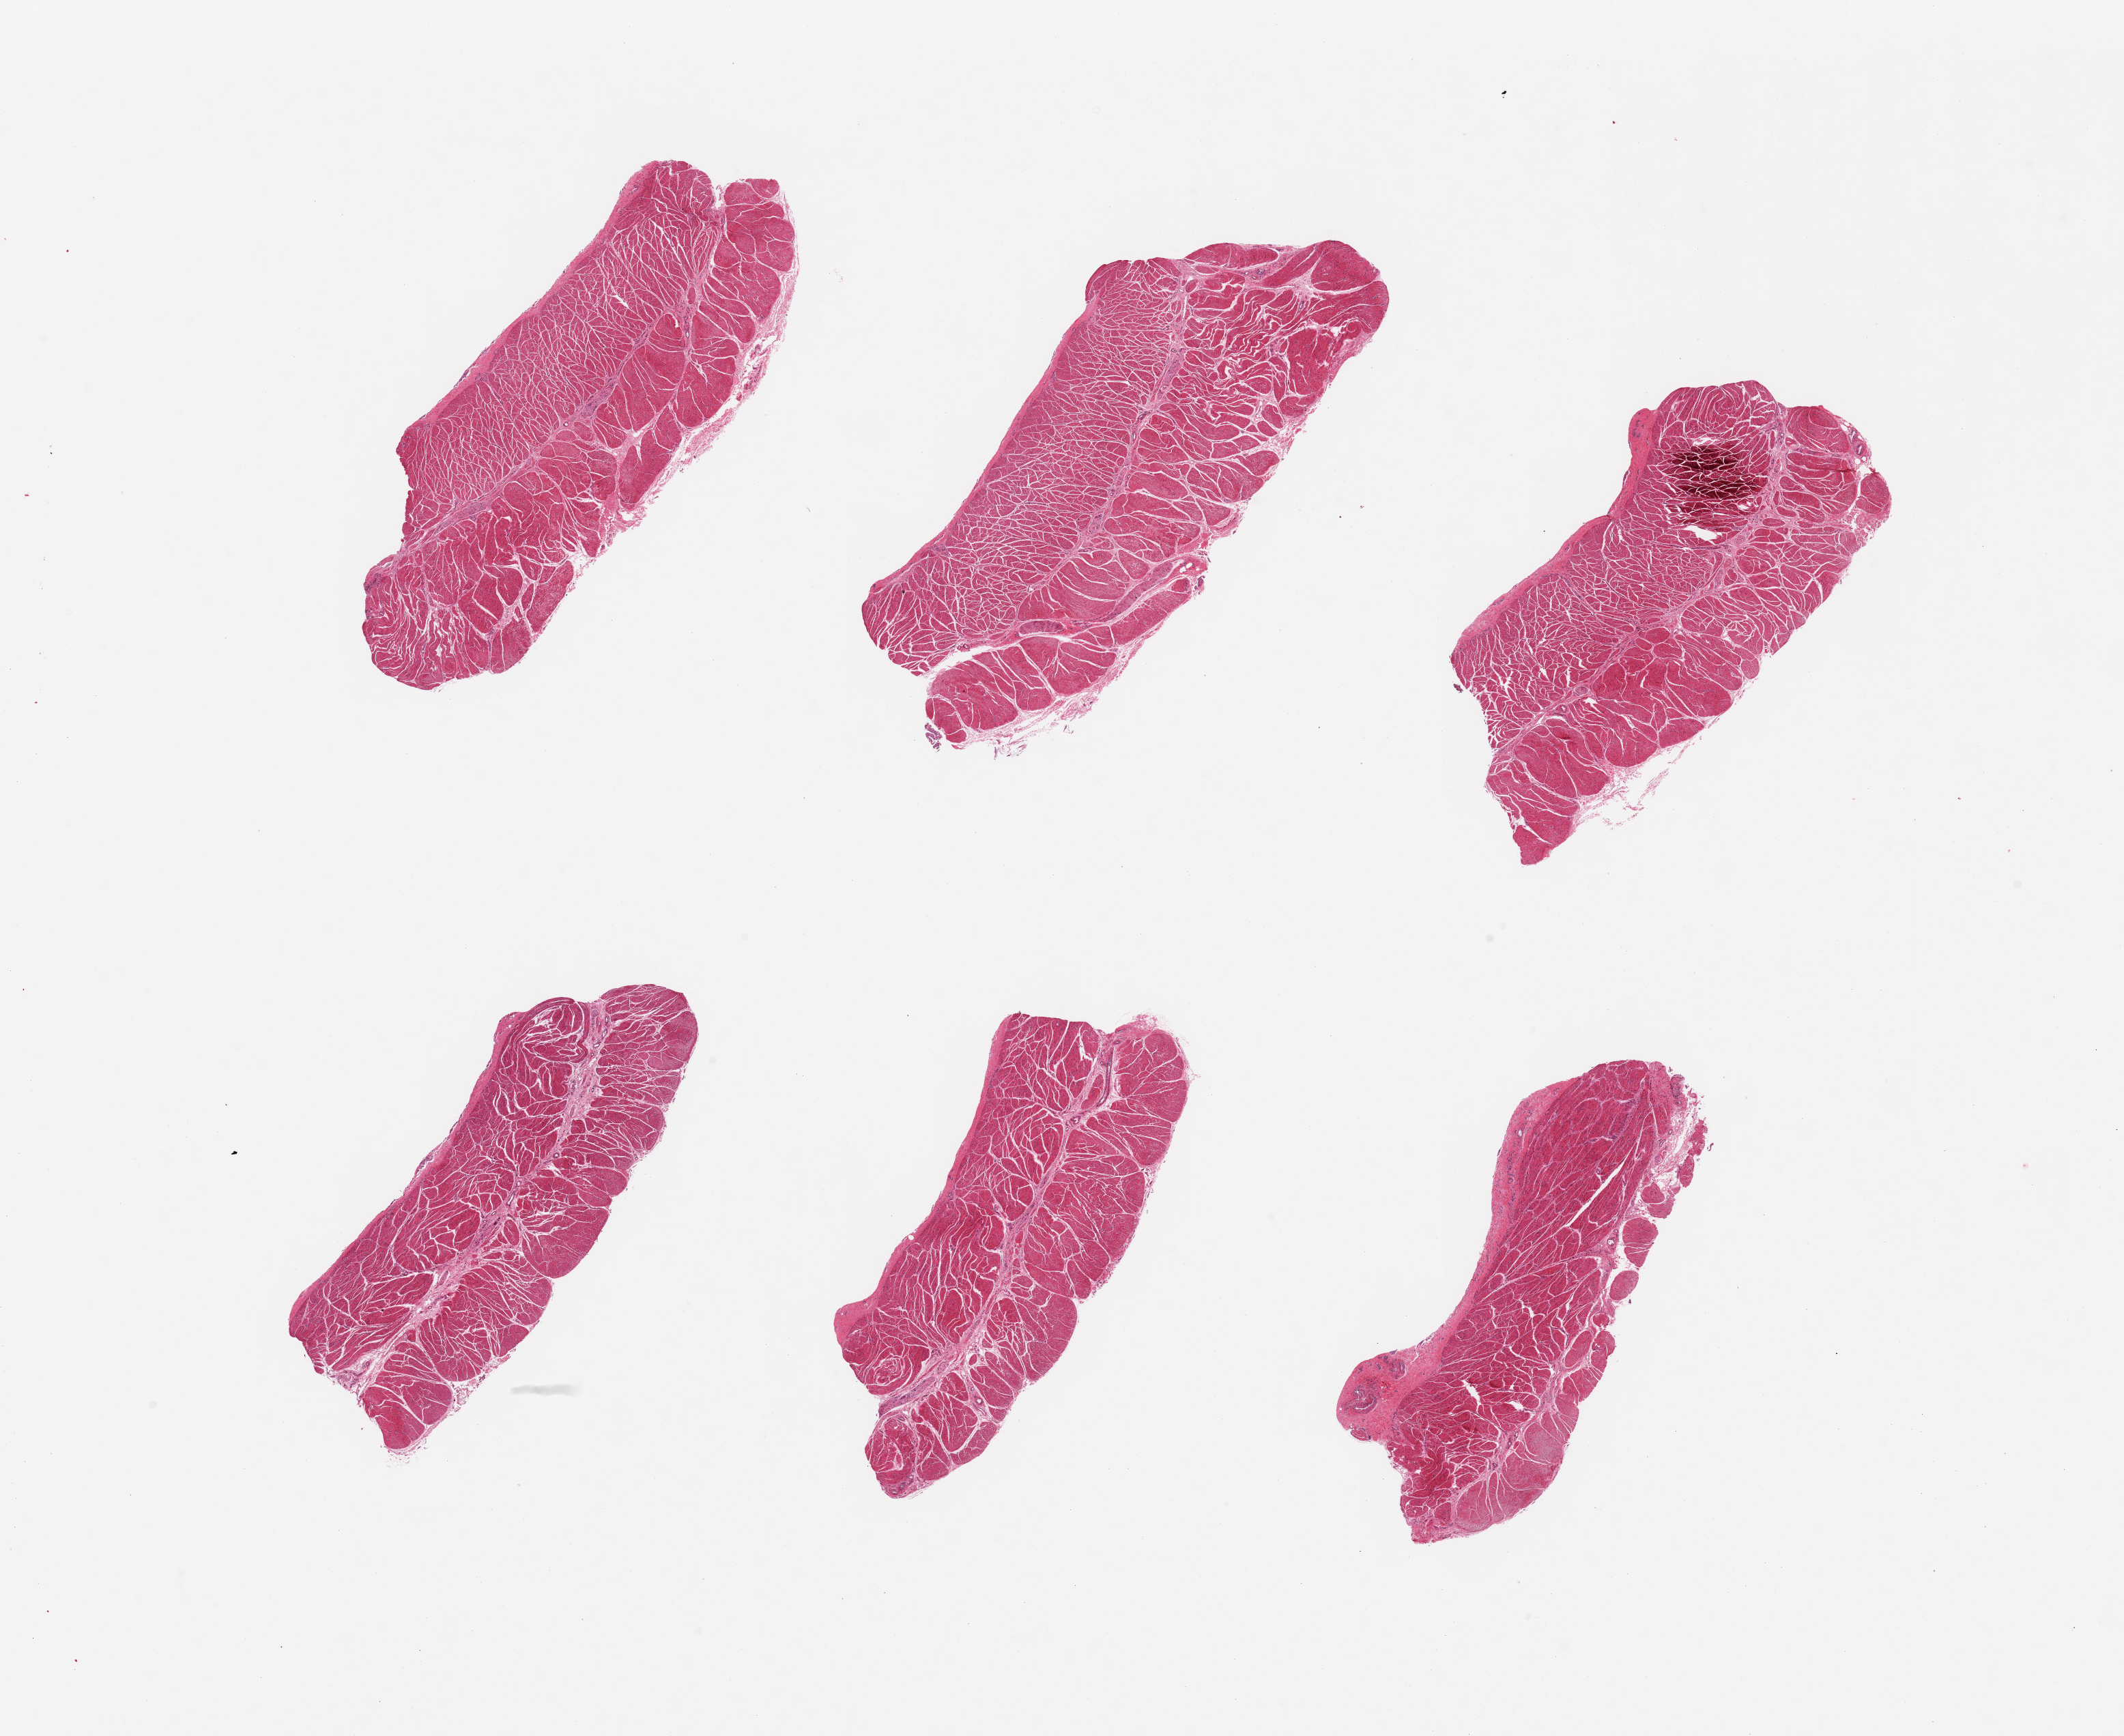
Hematoxylin and eosin (H&E) whole-slide image — whole scanned area (about 24.6 x 20.1 mm, from a 20x scan) shown as a low-resolution overview, PAXgene-fixed, paraffin-embedded tissue, section of esophageal muscle (target tissue), donor tissue sample.
- pathologist's review note for this sample: 6 pieces, confirmed target muscularis